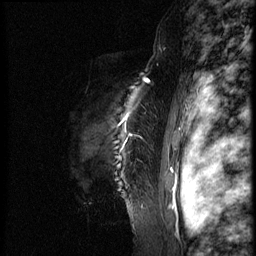
Breast MRI (dynamic contrast-enhanced), one sagittal slice; slice 59 of 66 in the series (ordered by position); dynamic contrast-enhanced series, image 2 of 3 at this slice position (ordered by acquisition); 1.5 T; TE 4.2 ms, TR 8.9 ms; 256 × 256 image matrix, field of view 200 × 200 mm. Female patient, age 39 years. Case-level facts recorded for this patient, not image findings: setting: breast cancer imaged before/during neoadjuvant chemotherapy; receptor status: HER2-positive.
Annotated regions visible in this slice (semi-automatic segmentation, software-assisted and operator-edited):
- analysis volume of interest (the breast-tissue region the enhancement analysis was run in; not a lesion): box from (x=69, y=75) to (x=160, y=218) px
- tumour enhancement mask (voxels above the 140 % enhancement threshold inside the analysis volume of interest): (x=147, y=80)–(x=149, y=83)